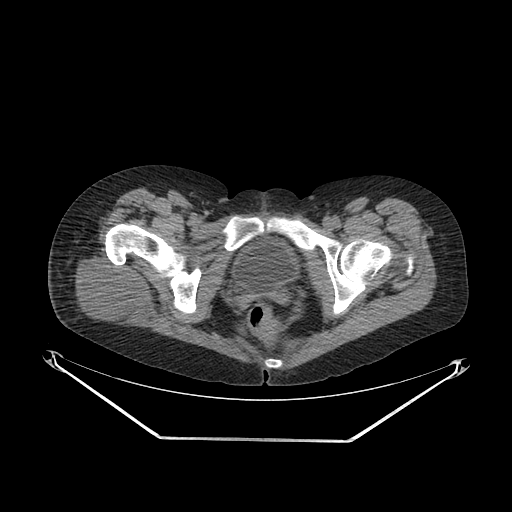
CT of an extremity soft-tissue mass (from a PET/CT study), one axial slice. Slice 45 of 267 in the series (ordered by position). Reconstruction kernel SOFT. 140 kVp. Soft-tissue window (W 400 / L 40 HU). 512 × 512 image matrix, field of view 500 × 500 mm. Female patient. From the clinical record (not read from this slice): histological type: epithelioid sarcoma with vascular differentiation; site of the primary tumour: right buttock.
Structures marked on this image (expert contour drawn on MRI and transferred to this co-registered scan by the dataset authors):
- gross tumour volume (mass): box from (x=66, y=247) to (x=154, y=334) px